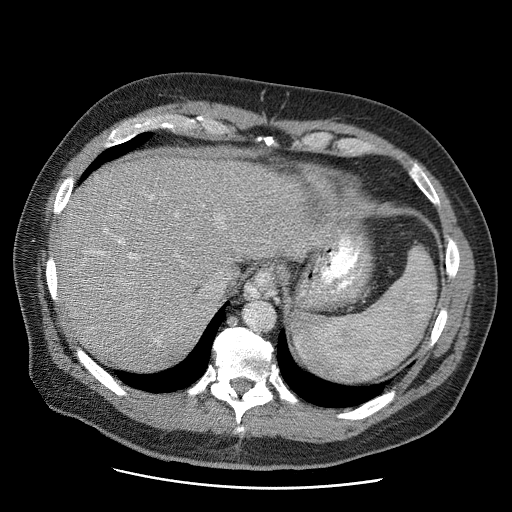
Contrast-enhanced abdominal CT (liver protocol), one axial slice; position 46 of 81 along the scan axis; 120 kVp; soft-tissue window (W 400 / L 40 HU); 512 × 512 image matrix. Case-level facts recorded for this patient, not image findings: diagnosis: hepatocellular carcinoma (patient treated with transarterial chemoembolisation; whether this scan precedes or follows treatment is not stated here); TNM stage (as recorded): Stage-IIIA; Child-Pugh class: A; tumour differentiation: moderately differentiated; tumour size: 5.5 cm.
Outlined on this slice (semi-automatically segmented with operator editing):
- liver parenchyma outside the tumour (the mass and vessels are separate outlines, so this box may not span the whole liver): bounding box <56,154,351,368> (left, top, right, bottom; pixels)
- liver vessels: <98,196,159,342>